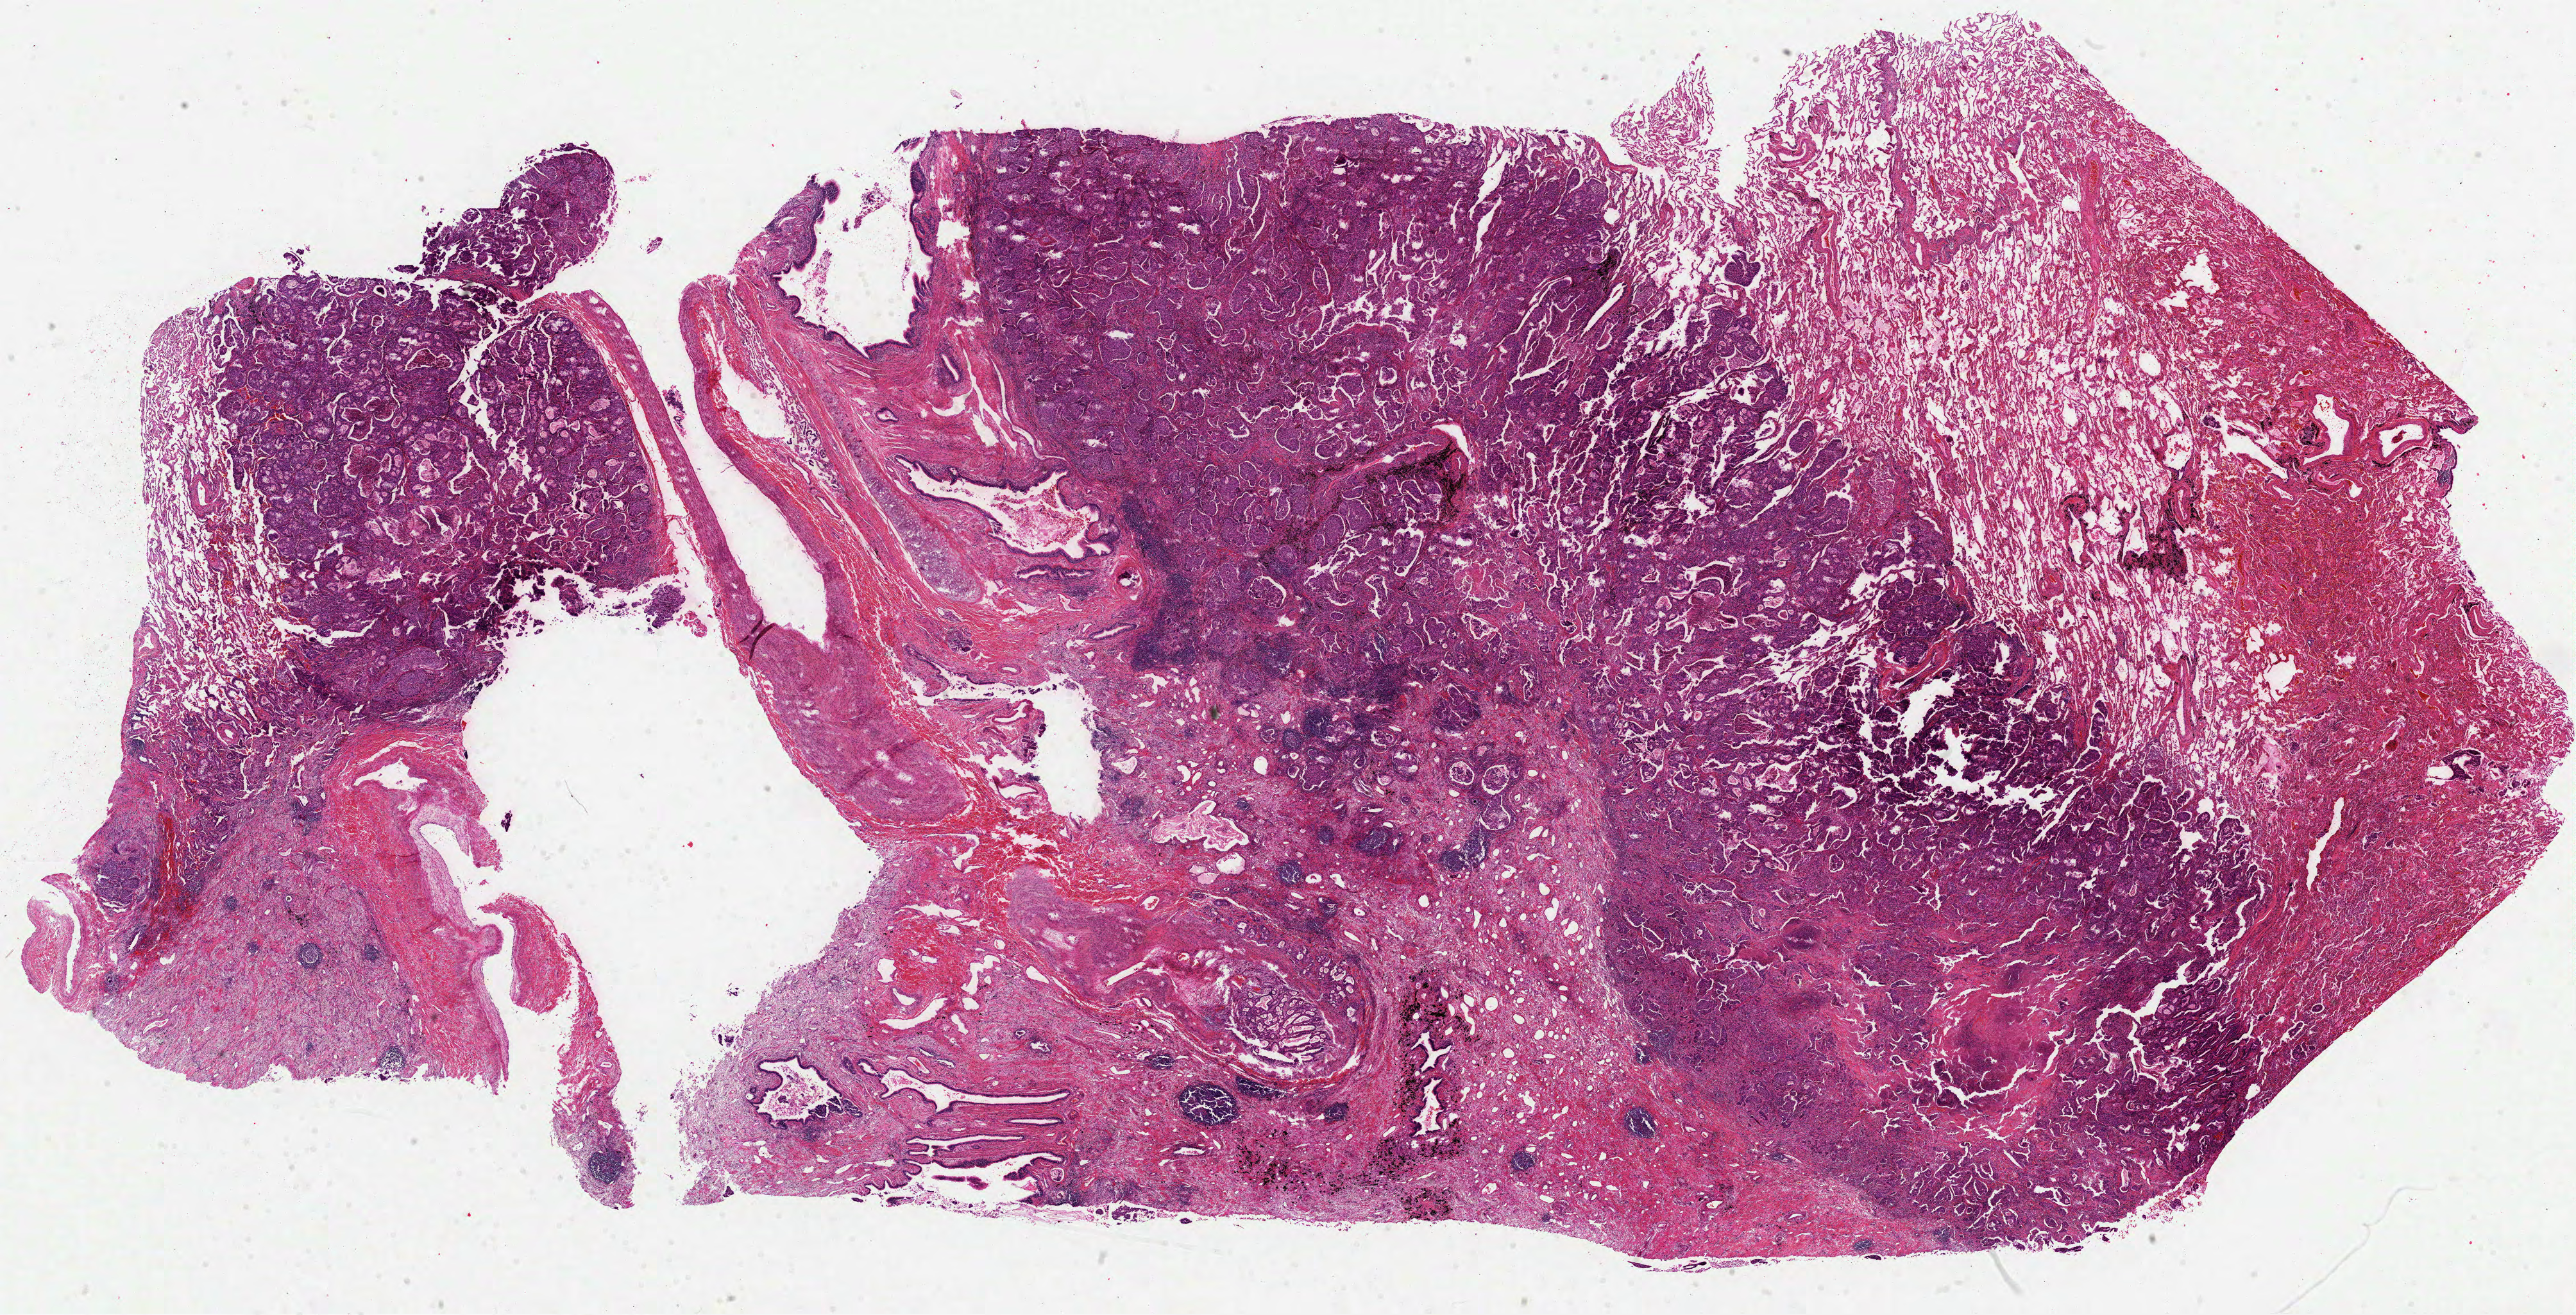
Whole-slide histology image, Hematoxylin and eosin (H&E) stained — shown as a low-resolution overview of the whole scanned area (about 32.4 x 16.5 mm, acquisition: 40x scan), formalin-fixed paraffin-embedded (FFPE) diagnostic section, lung, primary tumour sample. Patient: male, age at initial diagnosis 77 years.
- AJCC pathologic stage: IIIA (4th edition)
- diagnosis: Adenocarcinoma, NOS (upper lobe, lung)